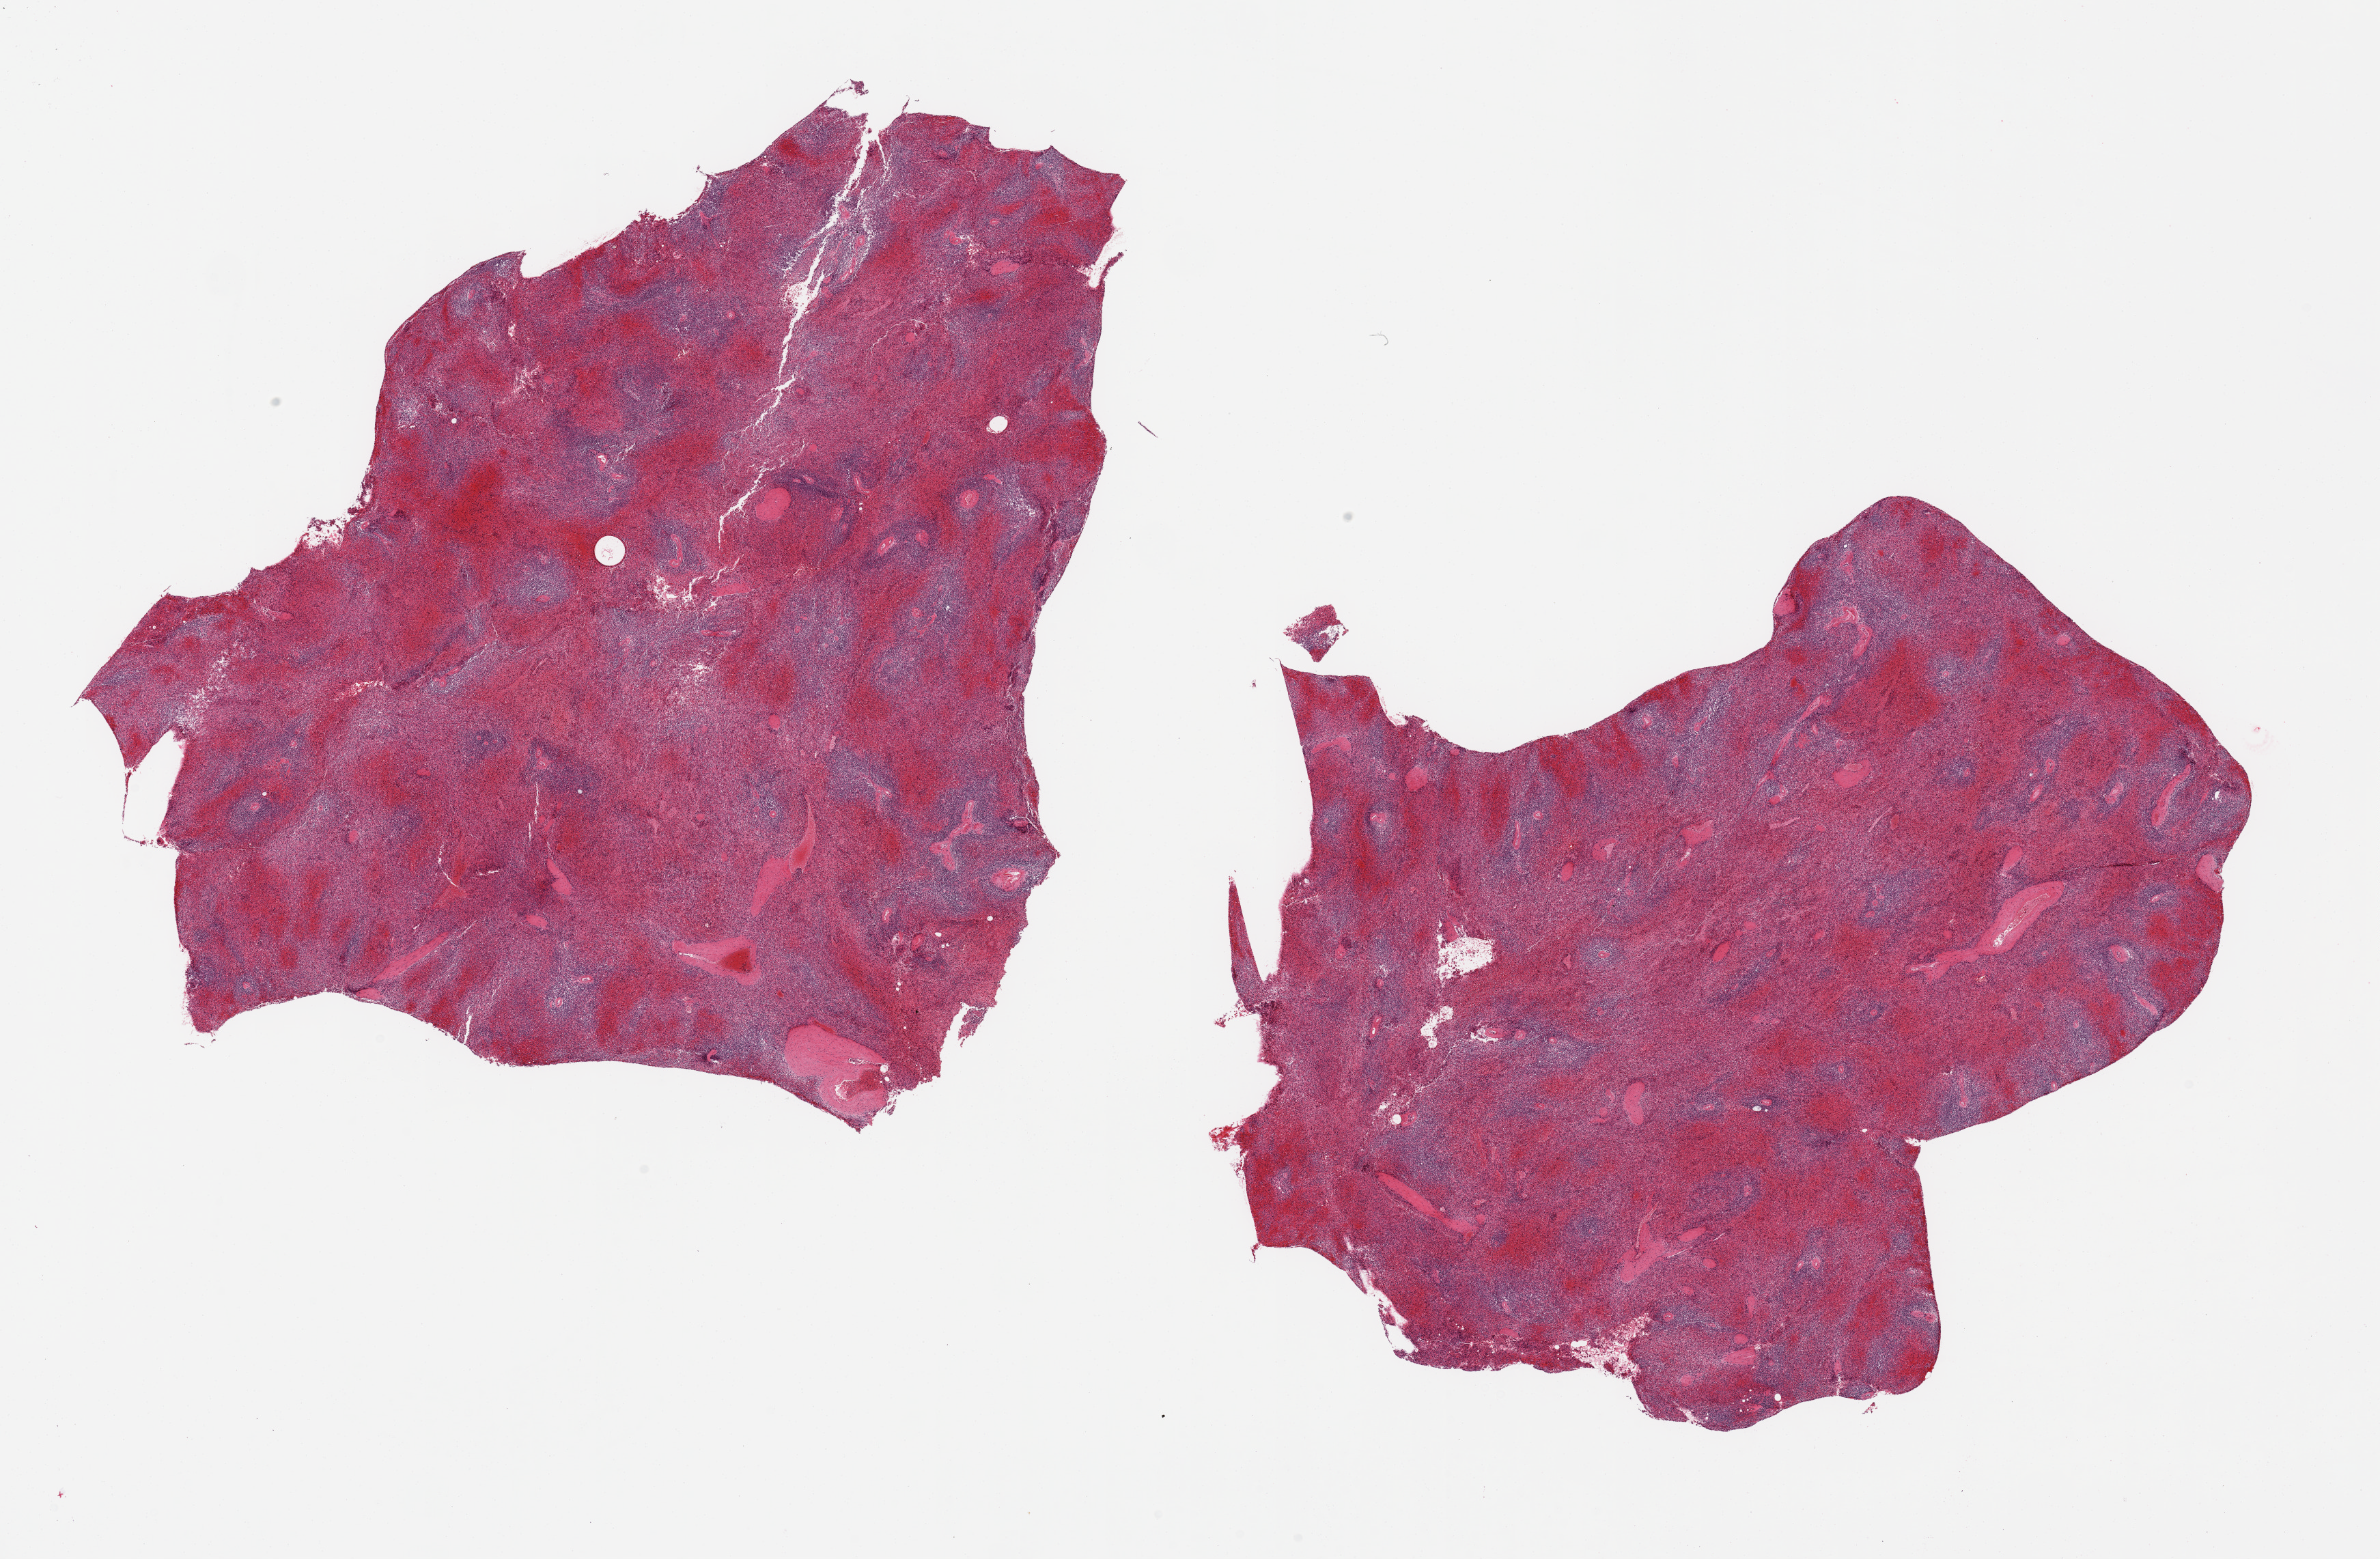
Digitized hematoxylin and eosin (H&E)-stained section, brightfield, whole scanned area (about 27.6 x 18.1 mm, from a 20x scan) shown as a low-resolution overview, PAXgene-fixed, paraffin-embedded tissue, target tissue: spleen, donor tissue sample. Donor: male.
Pathologist's review note for this sample: 2 pieces; moderately congested red pulp.